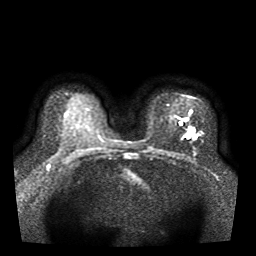
Breast MRI, one axial slice. Slice 24 of 41 in the series (ordered by position). Diffusion-weighted series; image 2 of 4 stored at this slice position (different b-values; order by instance number). 1.5 T. 5 mm slice thickness. 256 × 256 image matrix, field of view 330 × 330 mm. Female patient.
Outlined on this slice (manually delineated by an expert):
- tumour on diffusion-weighted imaging: bounding box (x1, y1, x2, y2) in pixels: (195, 136, 197, 138)